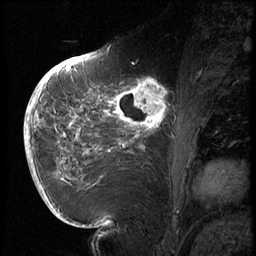
Breast MRI (dynamic contrast-enhanced), one sagittal slice; position 28 of 72 along the scan axis; 3 images stored at this slice position (order not interpretable as contrast timing); 1.5 T; TE 4.2 ms, TR 8.9 ms; 2.5 mm slice thickness; 256 × 256 image matrix, field of view 200 × 200 mm. Patient: female, 56 years. Case-level facts recorded for this patient, not image findings: setting: breast cancer imaged before/during neoadjuvant chemotherapy.
Annotated regions visible in this slice (semi-automatic segmentation, software-assisted and operator-edited):
- analysis volume of interest (the breast-tissue region the enhancement analysis was run in; not a lesion): box from (x=114, y=76) to (x=177, y=138) px
- tumour enhancement mask (voxels above the 140 % enhancement threshold inside the analysis volume of interest): (x=116, y=77)–(x=170, y=129)